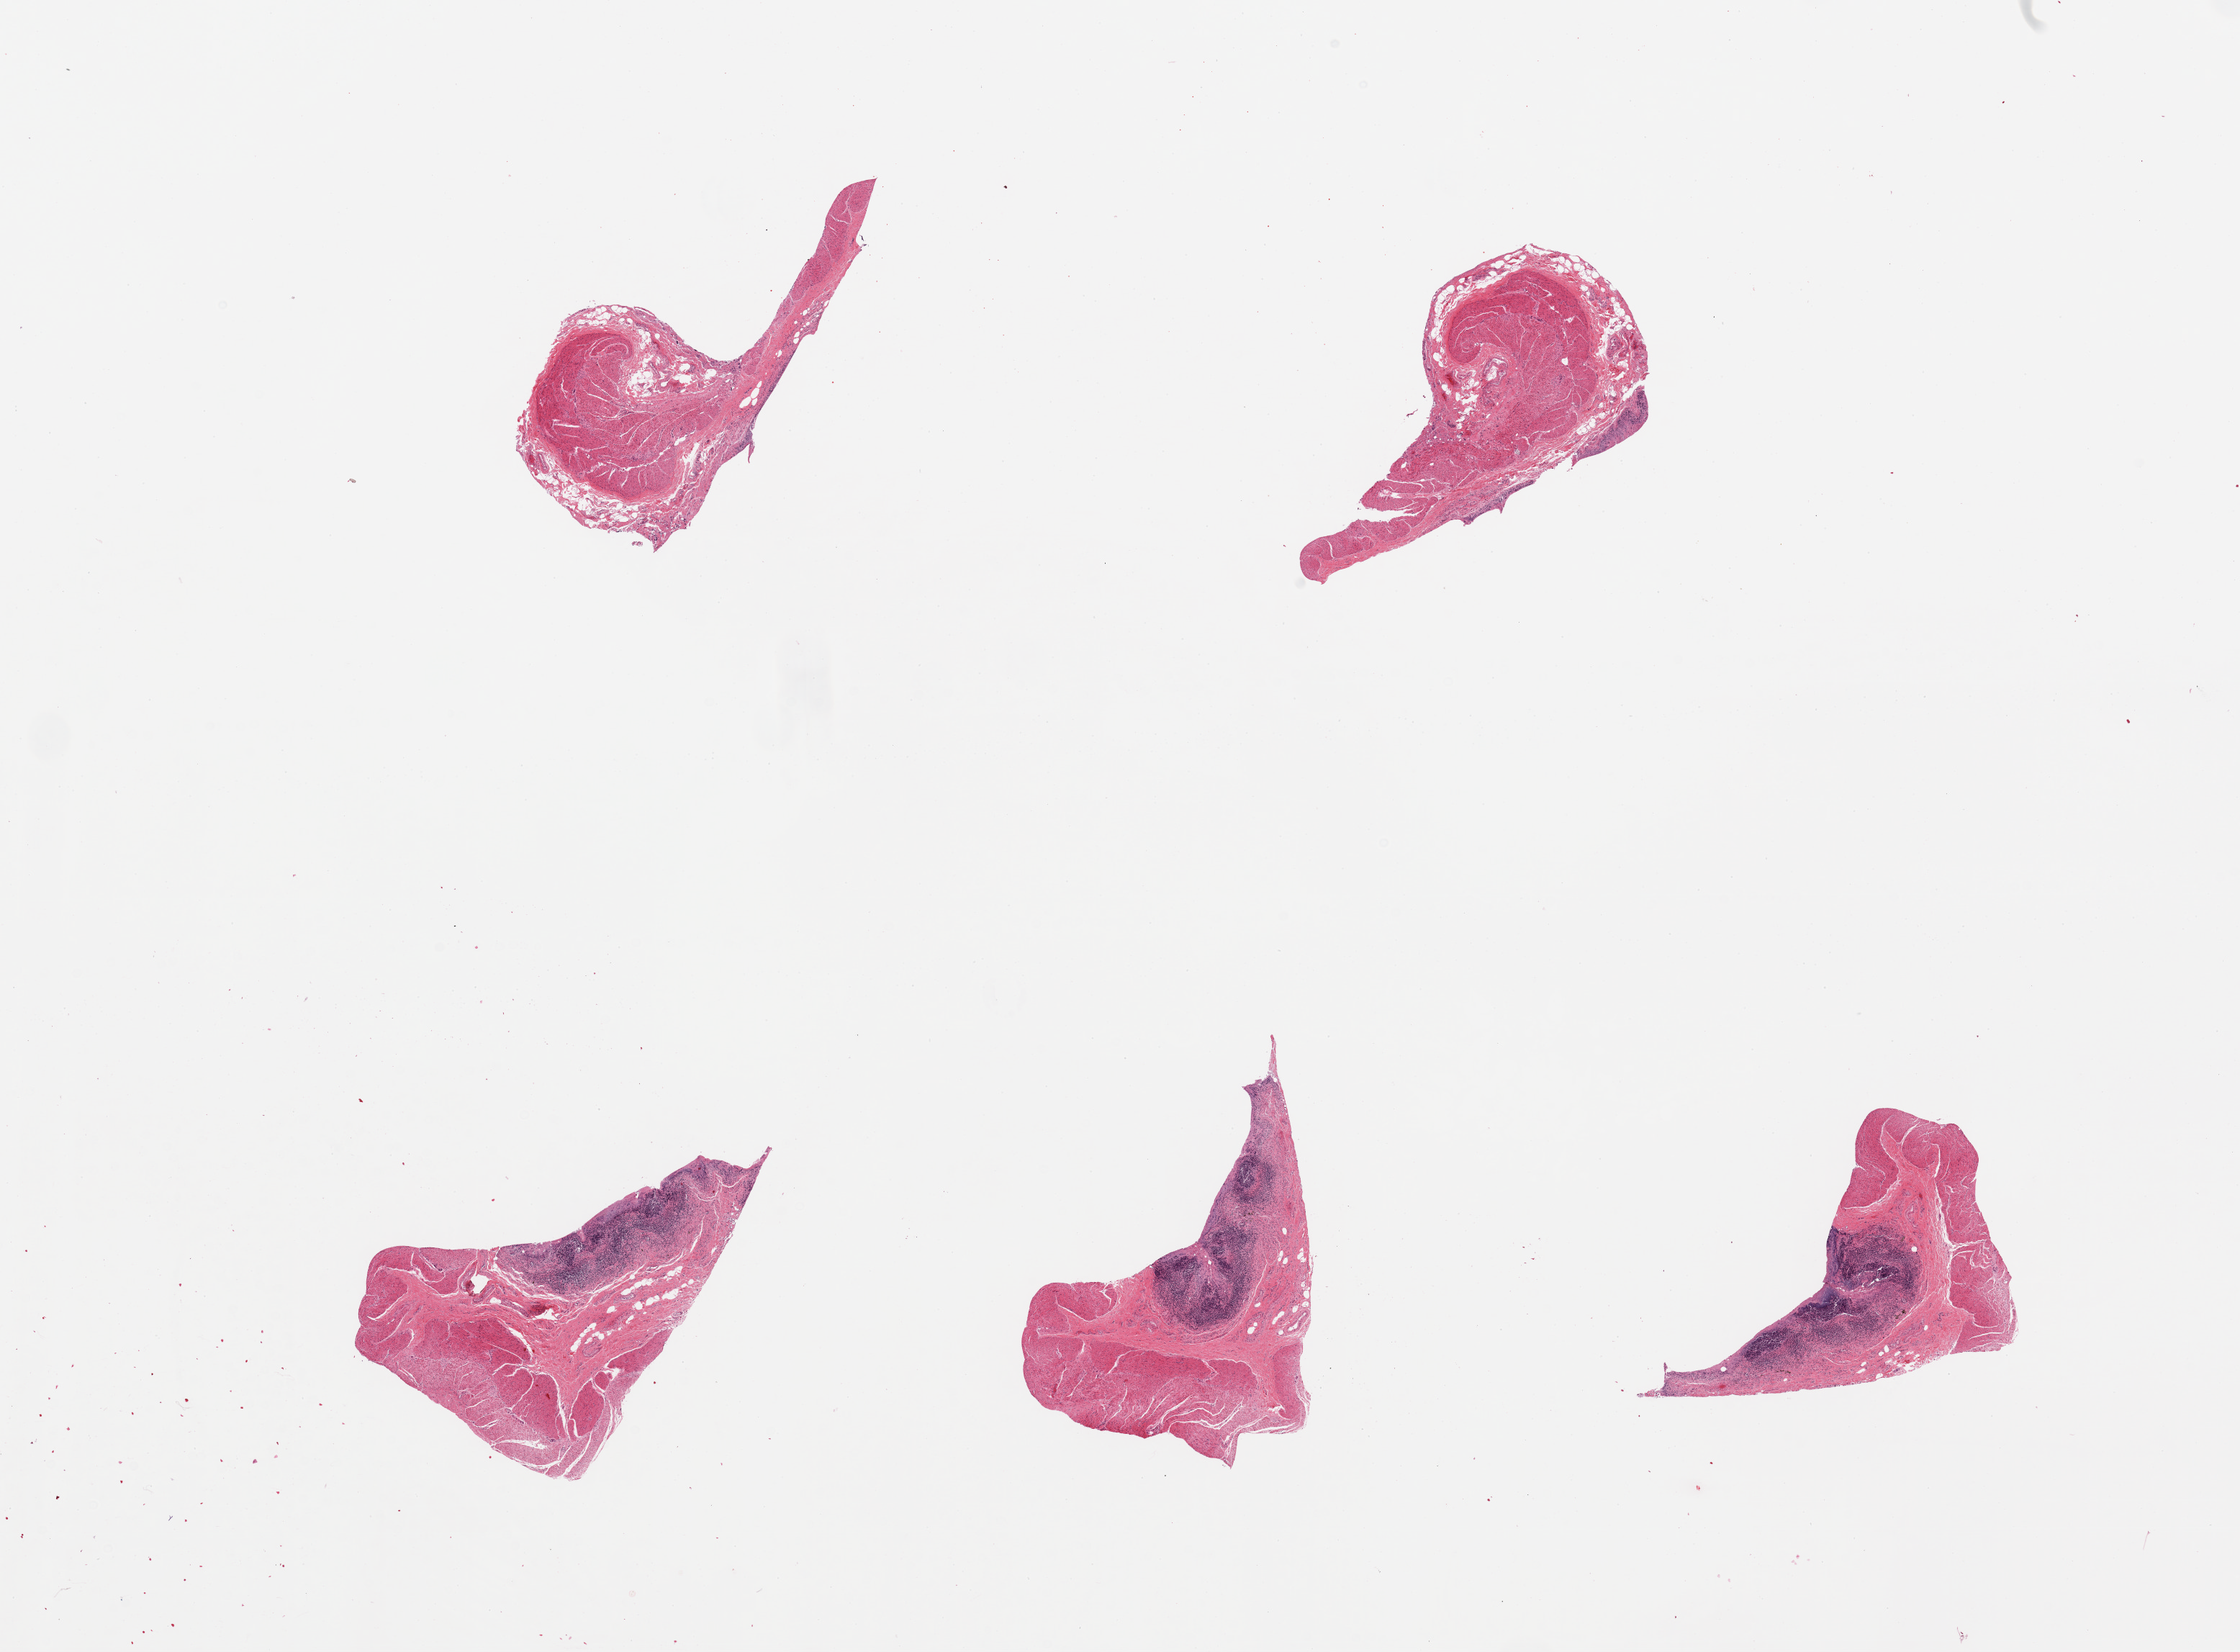
Digitized H&E-stained section, brightfield — whole scanned area (about 24.6 x 18.1 mm, acquisition: 20x scan) shown as a low-resolution overview. PAXgene-fixed paraffin-embedded (PFPE) section. Sampled site (target tissue): ileum. Tissue donor sample. Female donor.
- pathologist's review note for this sample: 5 pieces, mucosa totally sloughed, residual lymphoid aggregates are ~15% total tissue